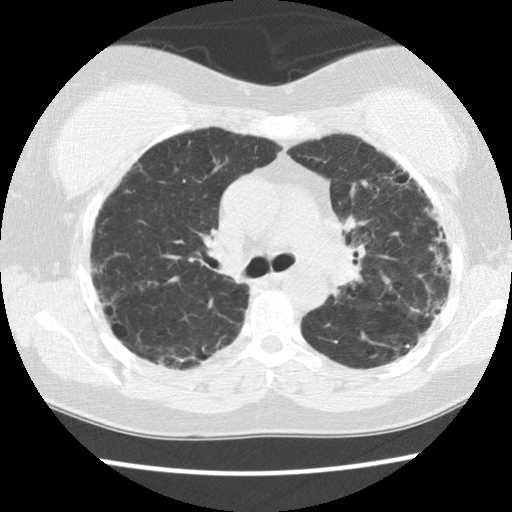
Low-dose screening chest CT, one axial slice. Slice 96 of 142 in the series (ordered by position). Reconstruction kernel STANDARD. Lung window (W 1500 / L -600 HU). 512 × 512 image matrix.
Outlined on this slice (manually delineated by an expert):
- lesion 1 (tumor): bounding box [x1, y1, x2, y2] px = [411, 308, 428, 315]